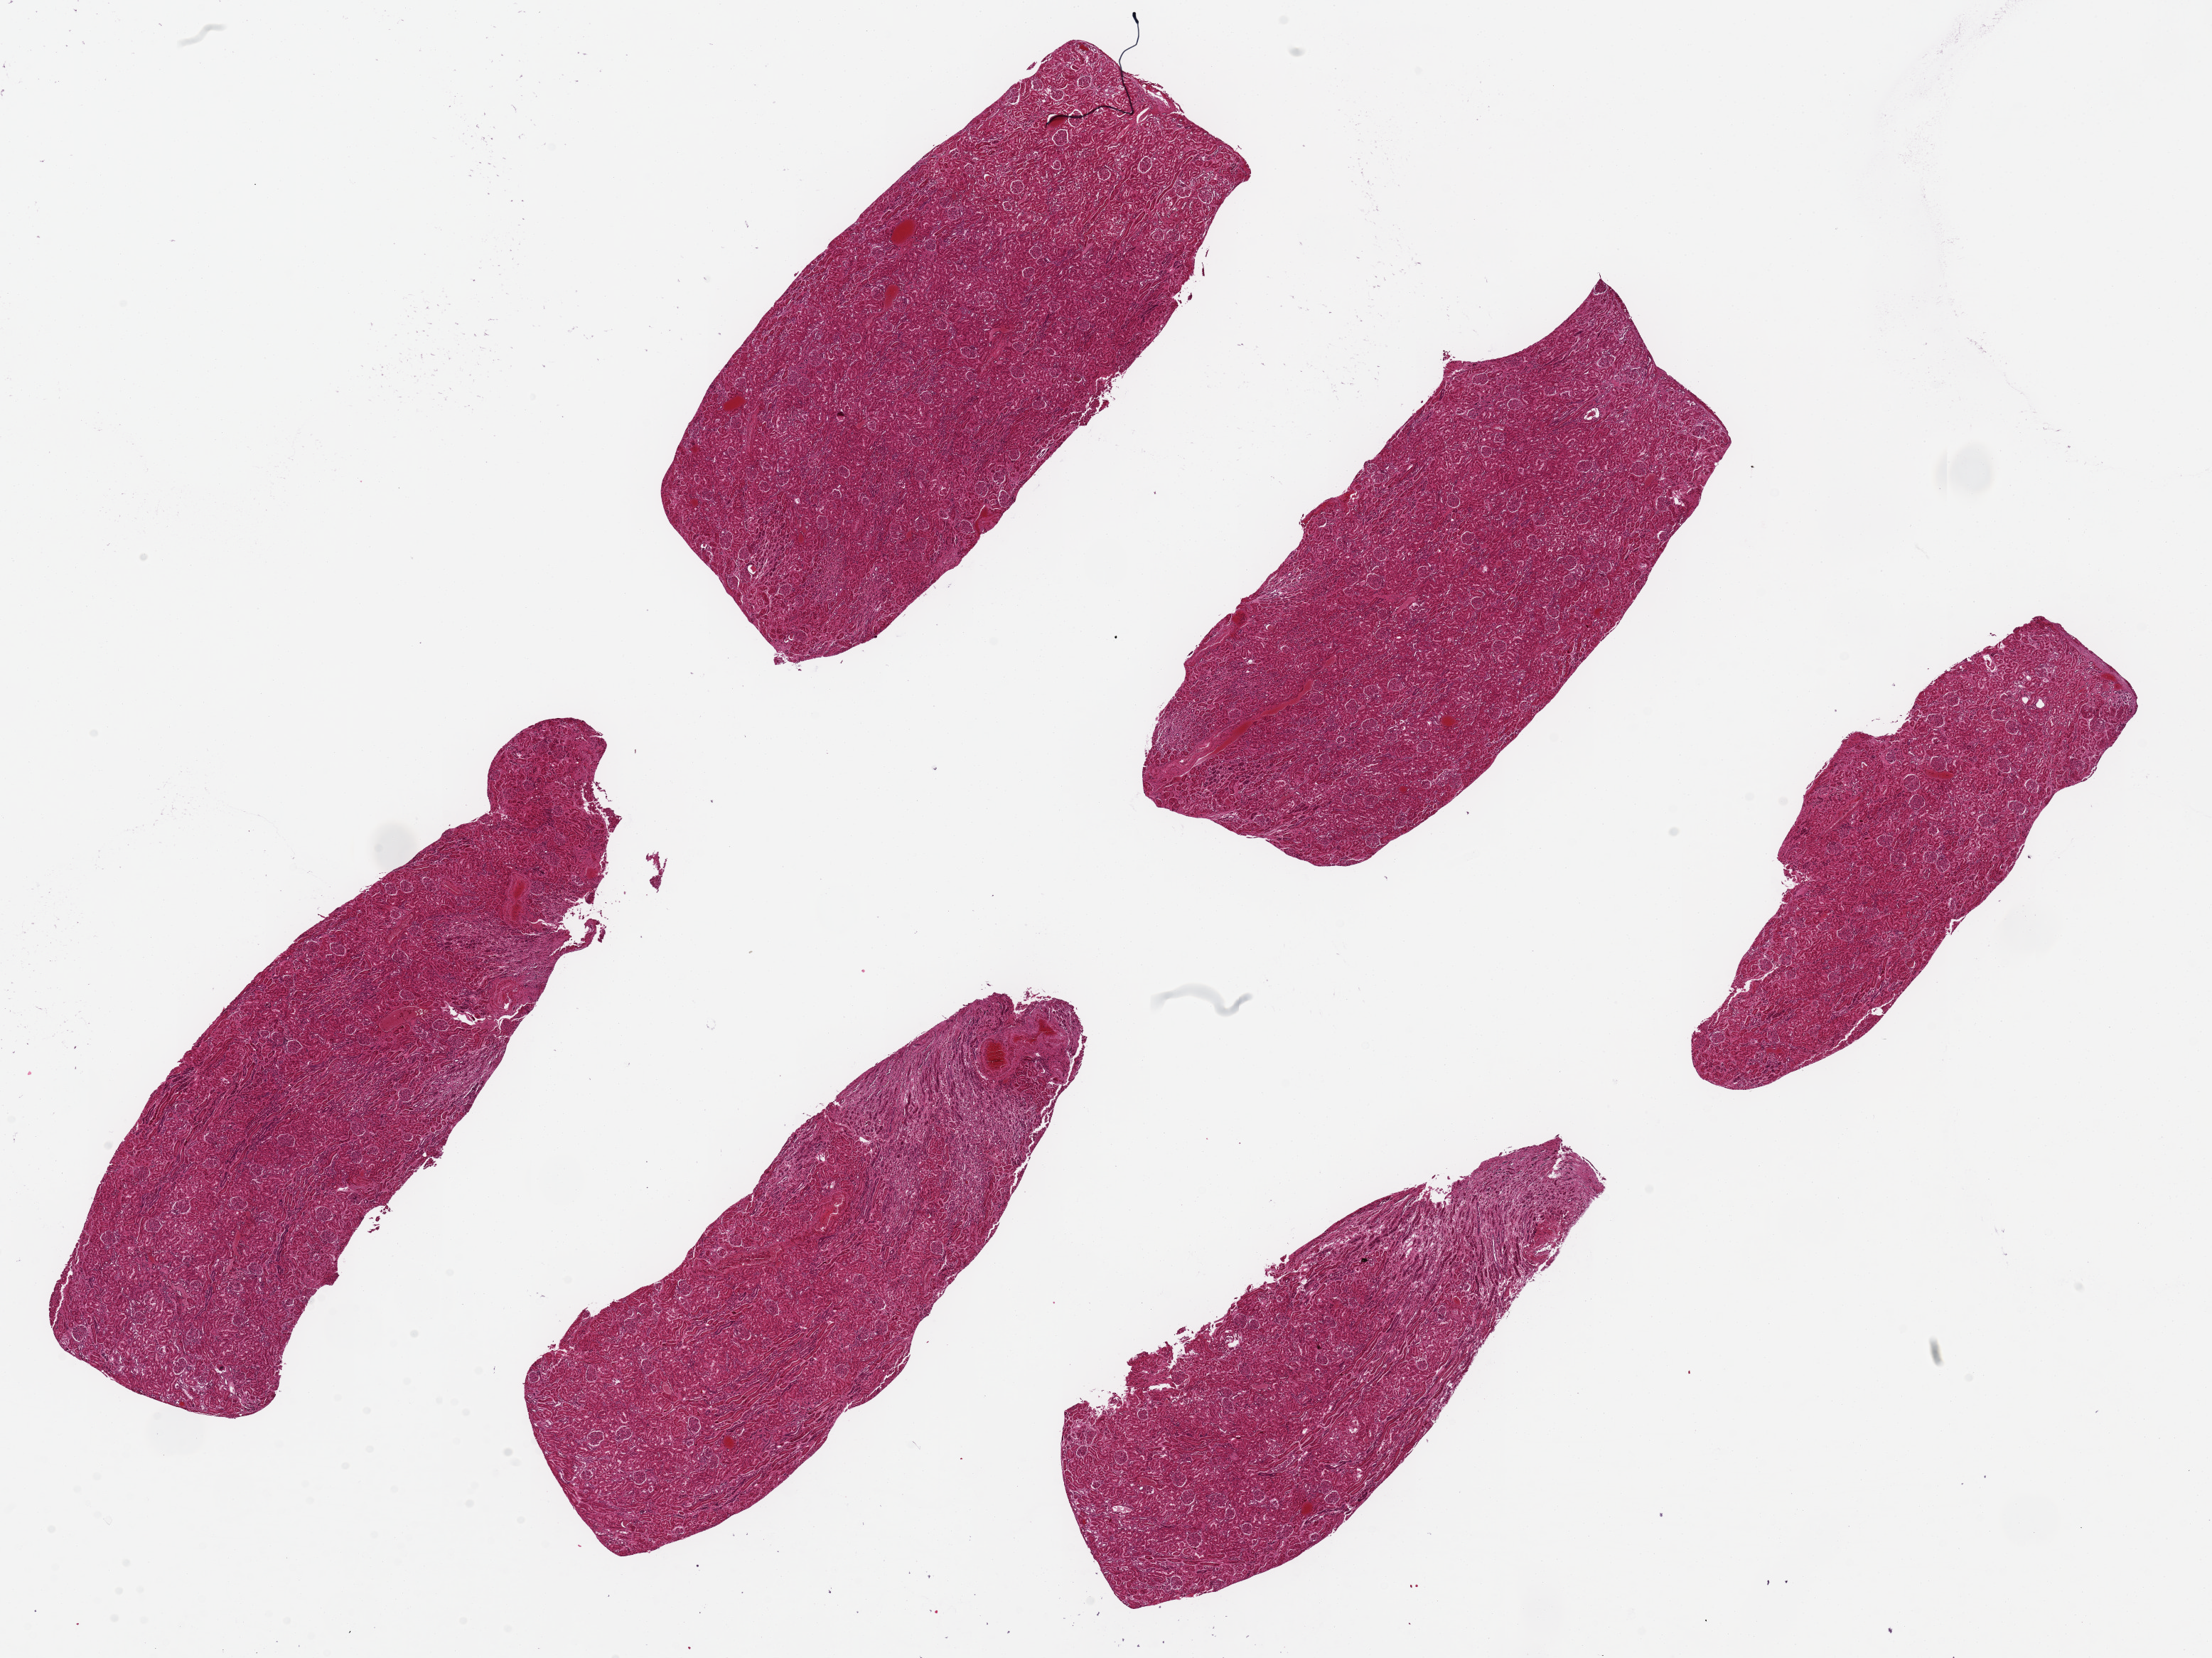
Hematoxylin and eosin (H&E) whole-slide image, whole scanned area (about 24.6 x 18.4 mm, from a 20x scan) shown as a low-resolution overview; PAXgene-fixed, paraffin-embedded tissue; section of renal cortex (target tissue); tissue donor sample. Donor sex: male.
Reviewer comment on this tissue sample: 6 pieces, 7x3mm.